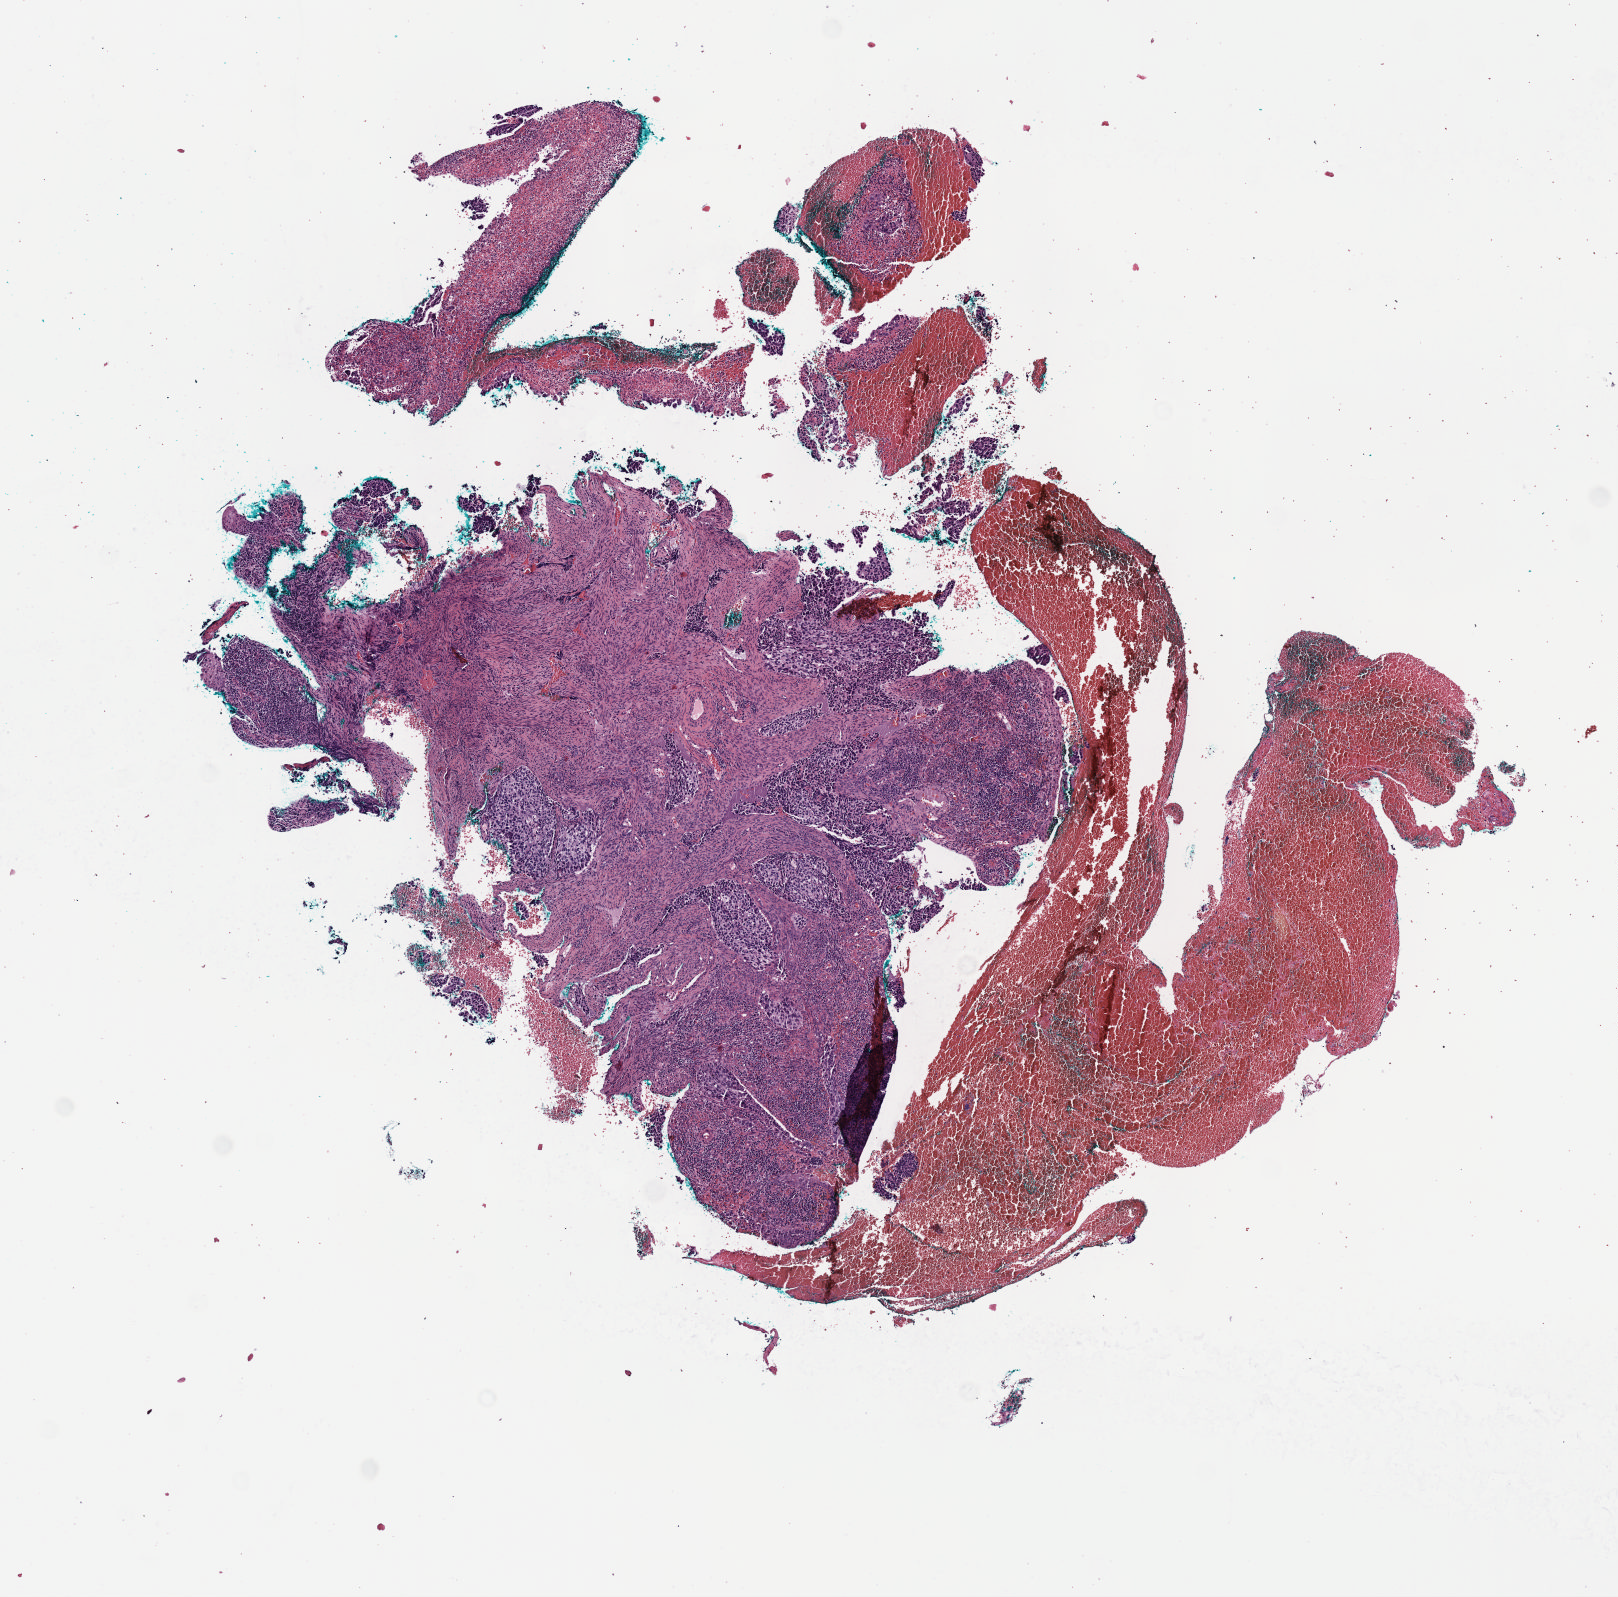
Whole-slide histology image, H&E-stained, whole scanned area (about 6.5 x 6.5 mm, from a 40x scan) shown as a low-resolution overview; formalin-fixed paraffin-embedded (FFPE) diagnostic section; sample: primary tumour, cervix. Patient: female, age at initial diagnosis 43 years. Histologic grade: G3 (poorly differentiated).
Pathologic diagnosis: Mucinous adenocarcinoma, endocervical type (cervix uteri). FIGO stage: IIA.